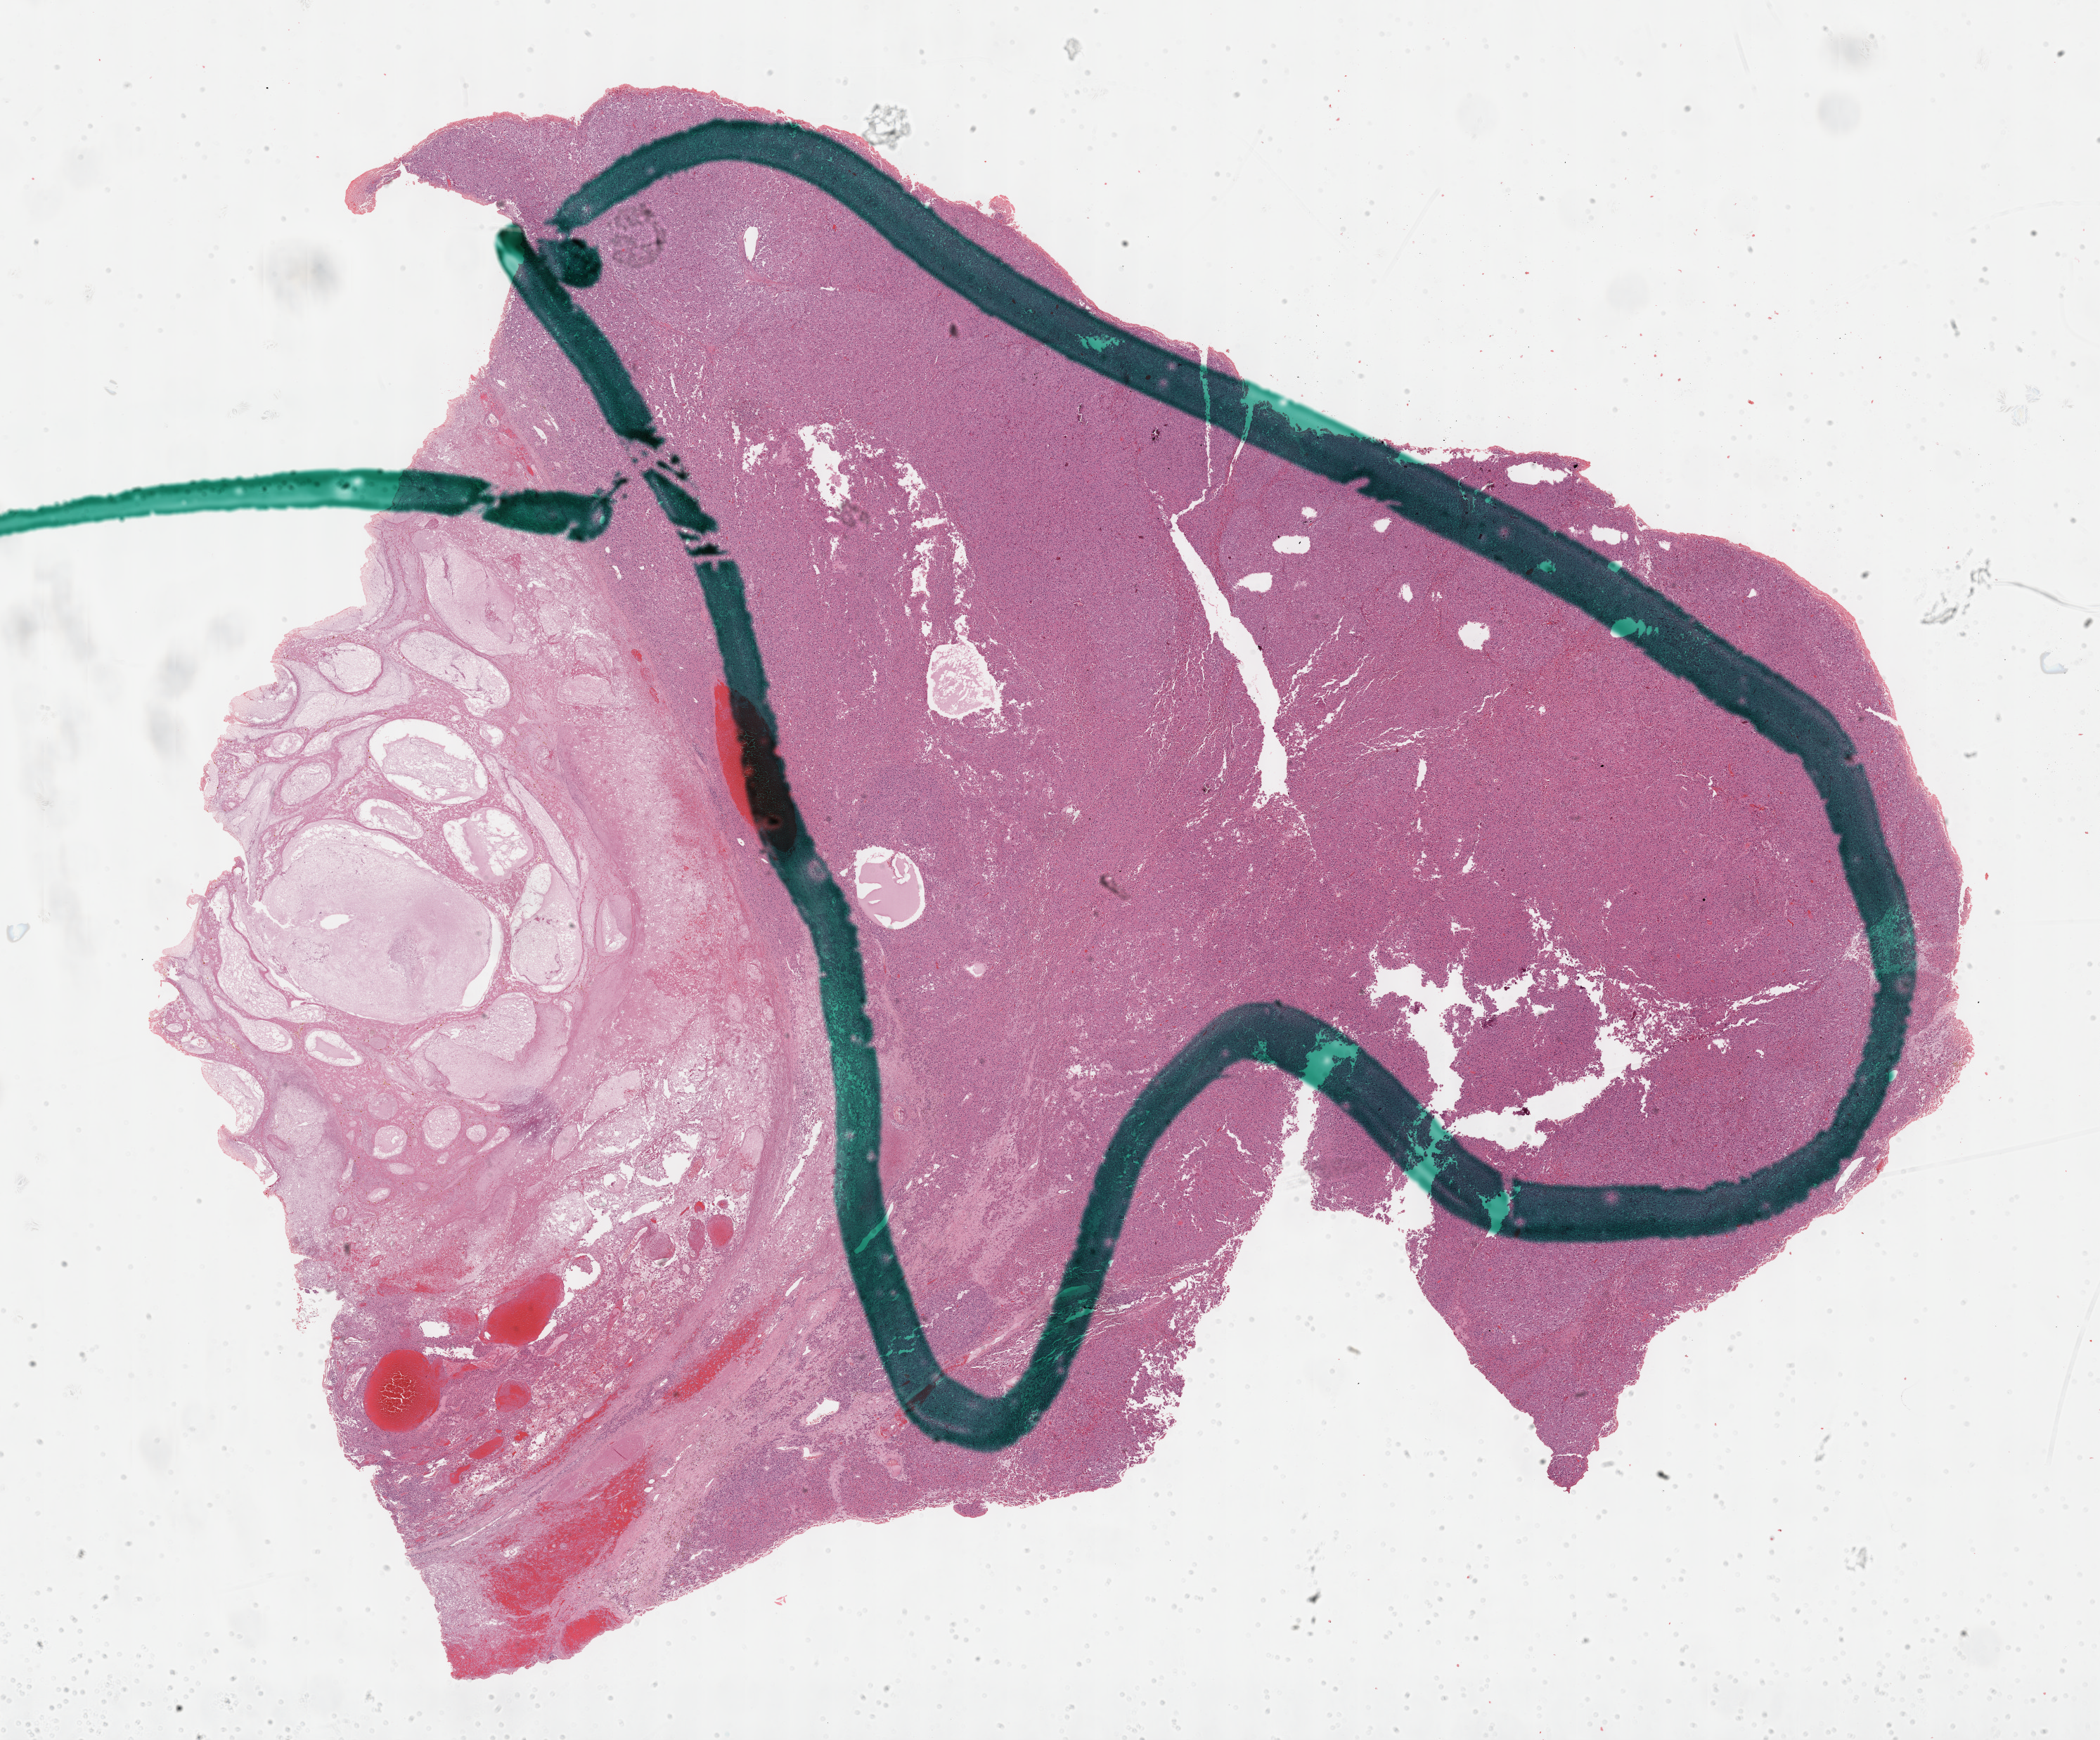
H&E whole-slide image, shown as a low-resolution overview of the whole scanned area (about 24.2 x 20.0 mm, from a 40x scan), FFPE section, primary tumour sample from the adrenal cortex. Male patient; age at initial diagnosis 53 years.
Histologic diagnosis: Adrenal cortical carcinoma (cortex of adrenal gland).